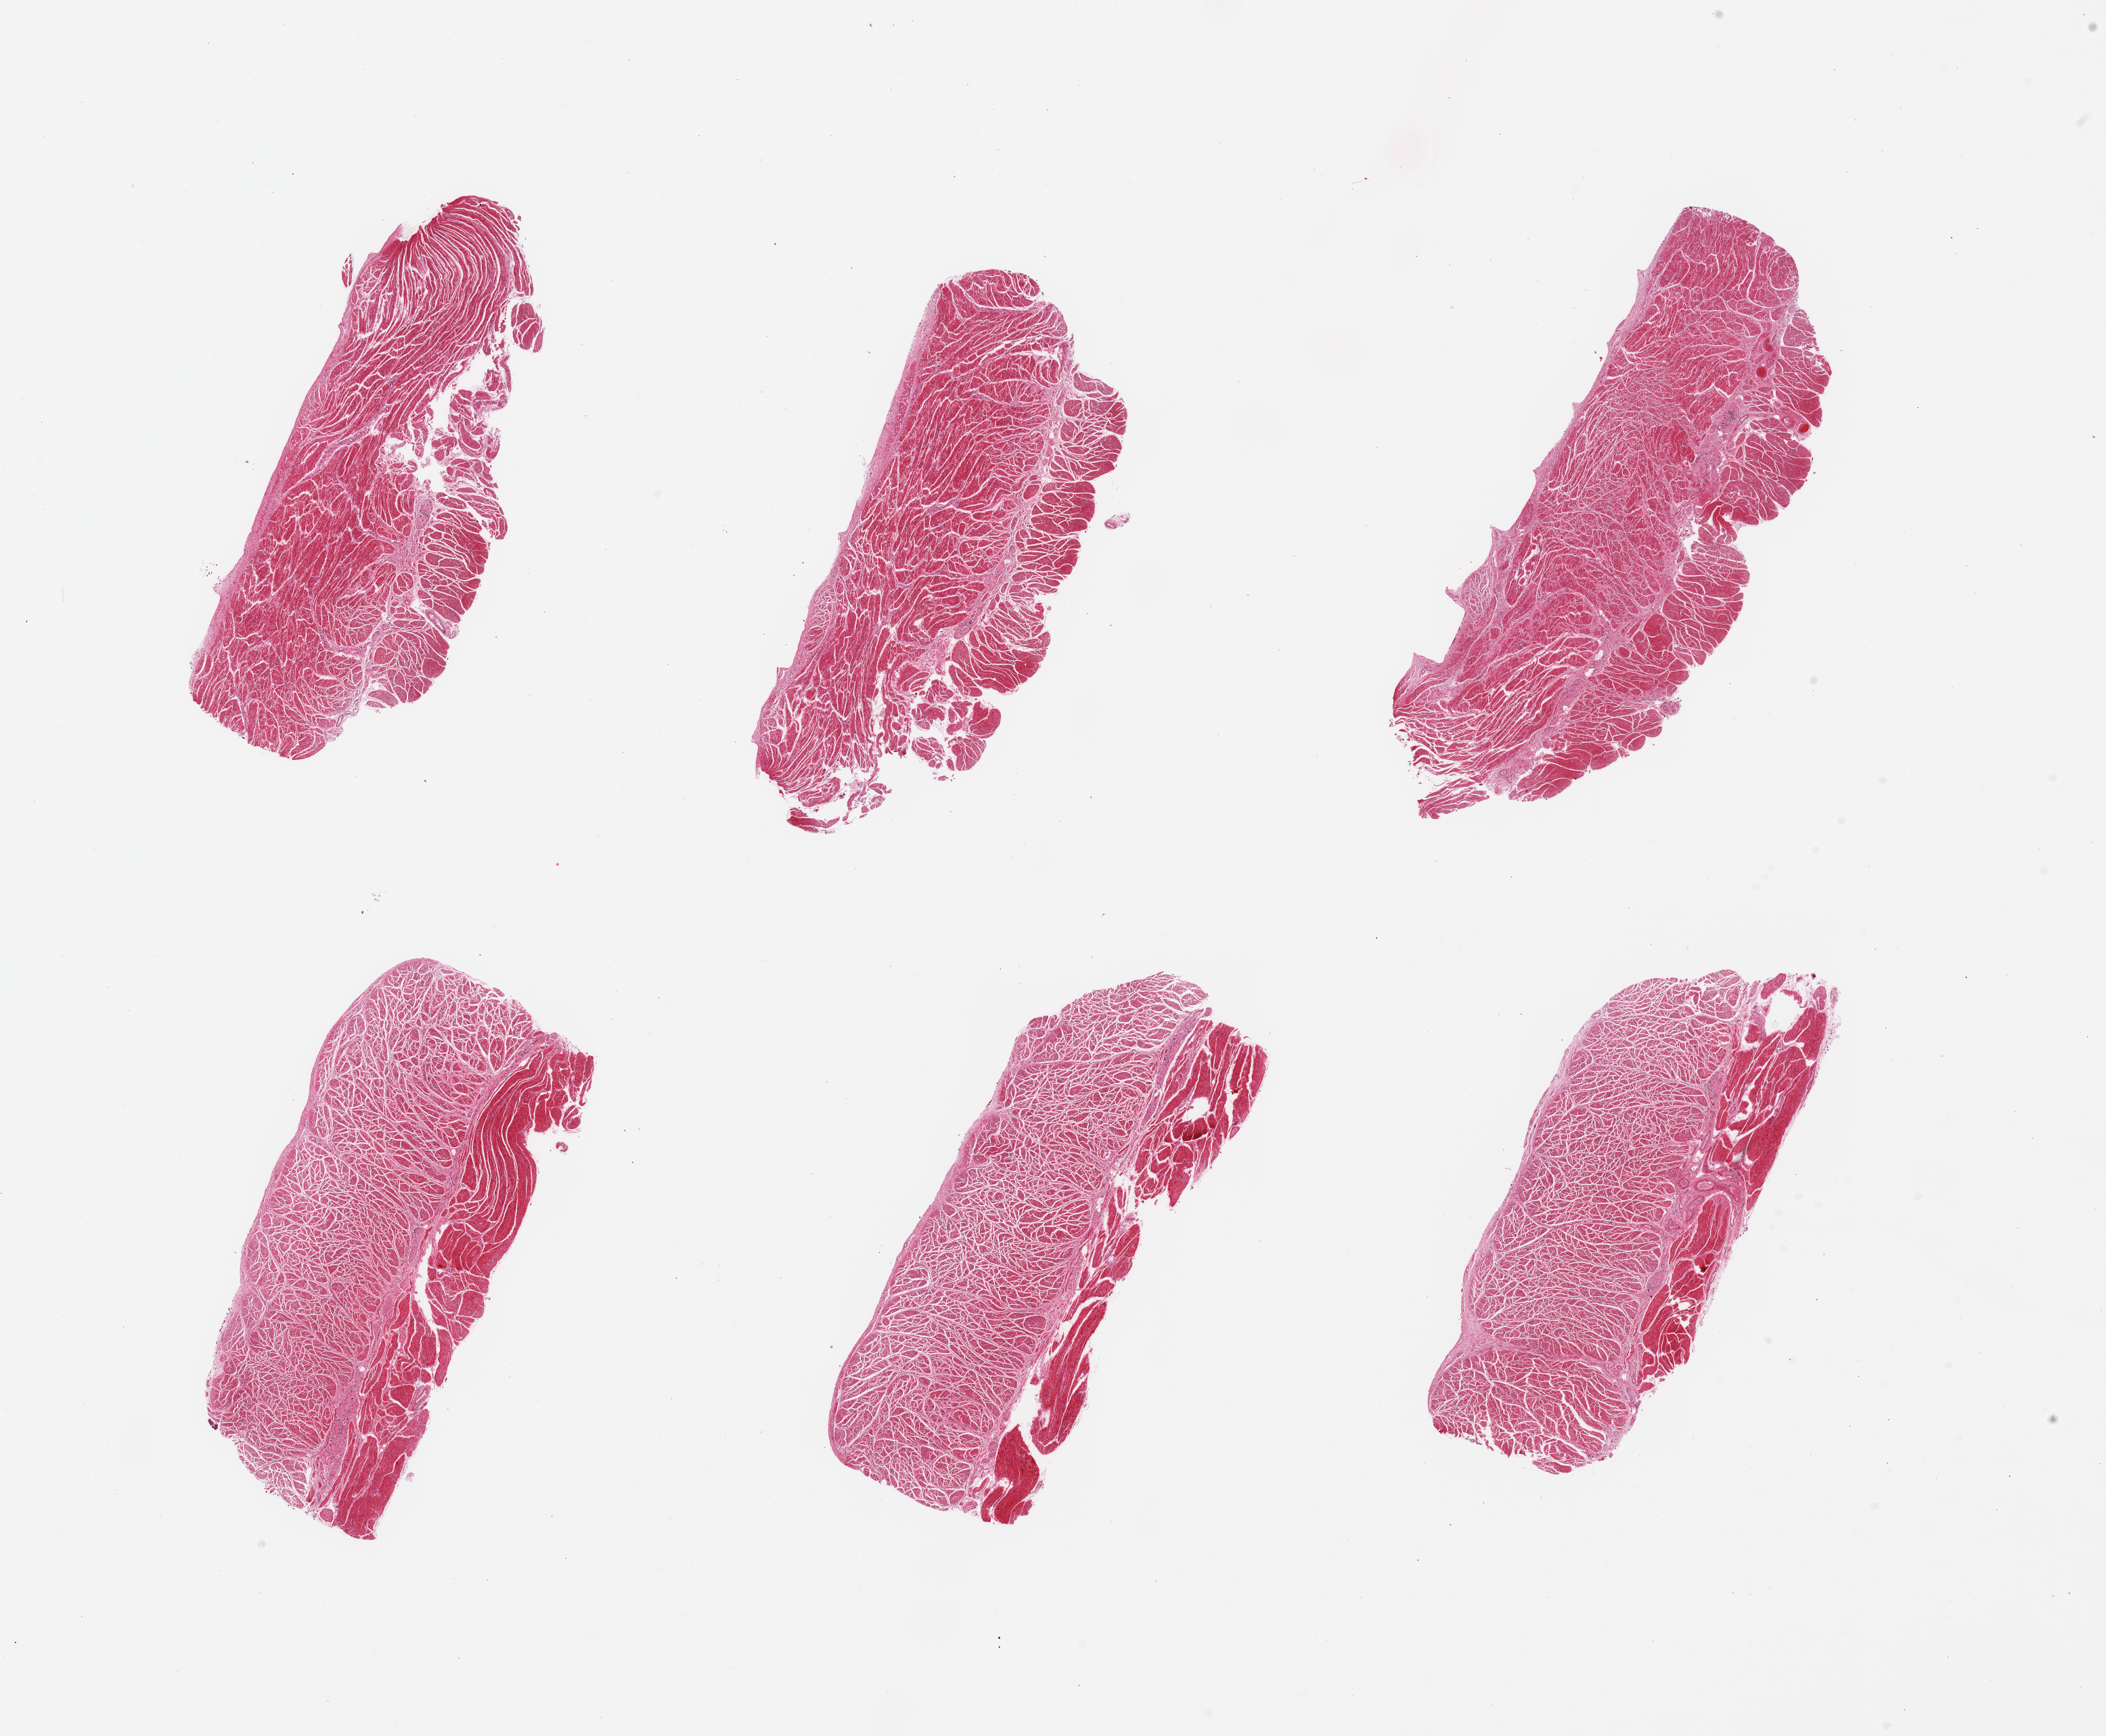
Hematoxylin and eosin (H&E) whole-slide image — shown as a low-resolution overview of the whole scanned area (about 24.6 x 20.3 mm, slide scanned at 20x), PAXgene-fixed, paraffin-embedded tissue, target tissue: esophageal muscle, tissue donor sample. Donor: female.
Review note (as recorded): 6 pieces; well dissected.